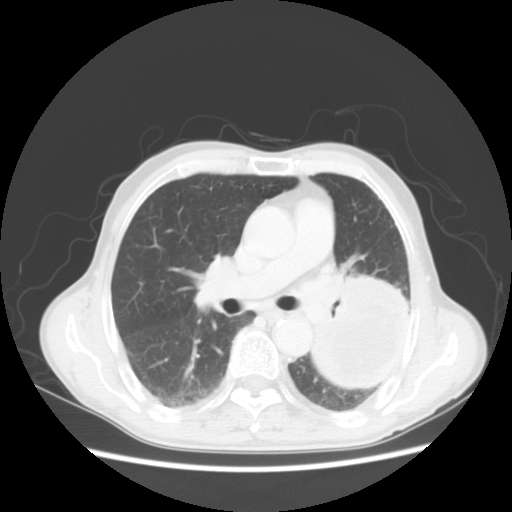
Chest CT, one axial slice. Position 30 of 51 along the scan axis. Reconstruction kernel STANDARD. Lung window (W 1500 / L -600 HU). 512 × 512 image matrix, field of view 360 × 360 mm. Patient: male, 64 years. From the clinical record (not read from this slice): clinical TNM (as recorded): T4 N0 M0.
Structures marked on this image (rectangle marked by the reading radiologist):
- lung tumour (recorded histology: squamous cell carcinoma): bounding box (x1, y1, x2, y2) in pixels: (312, 262, 419, 400)